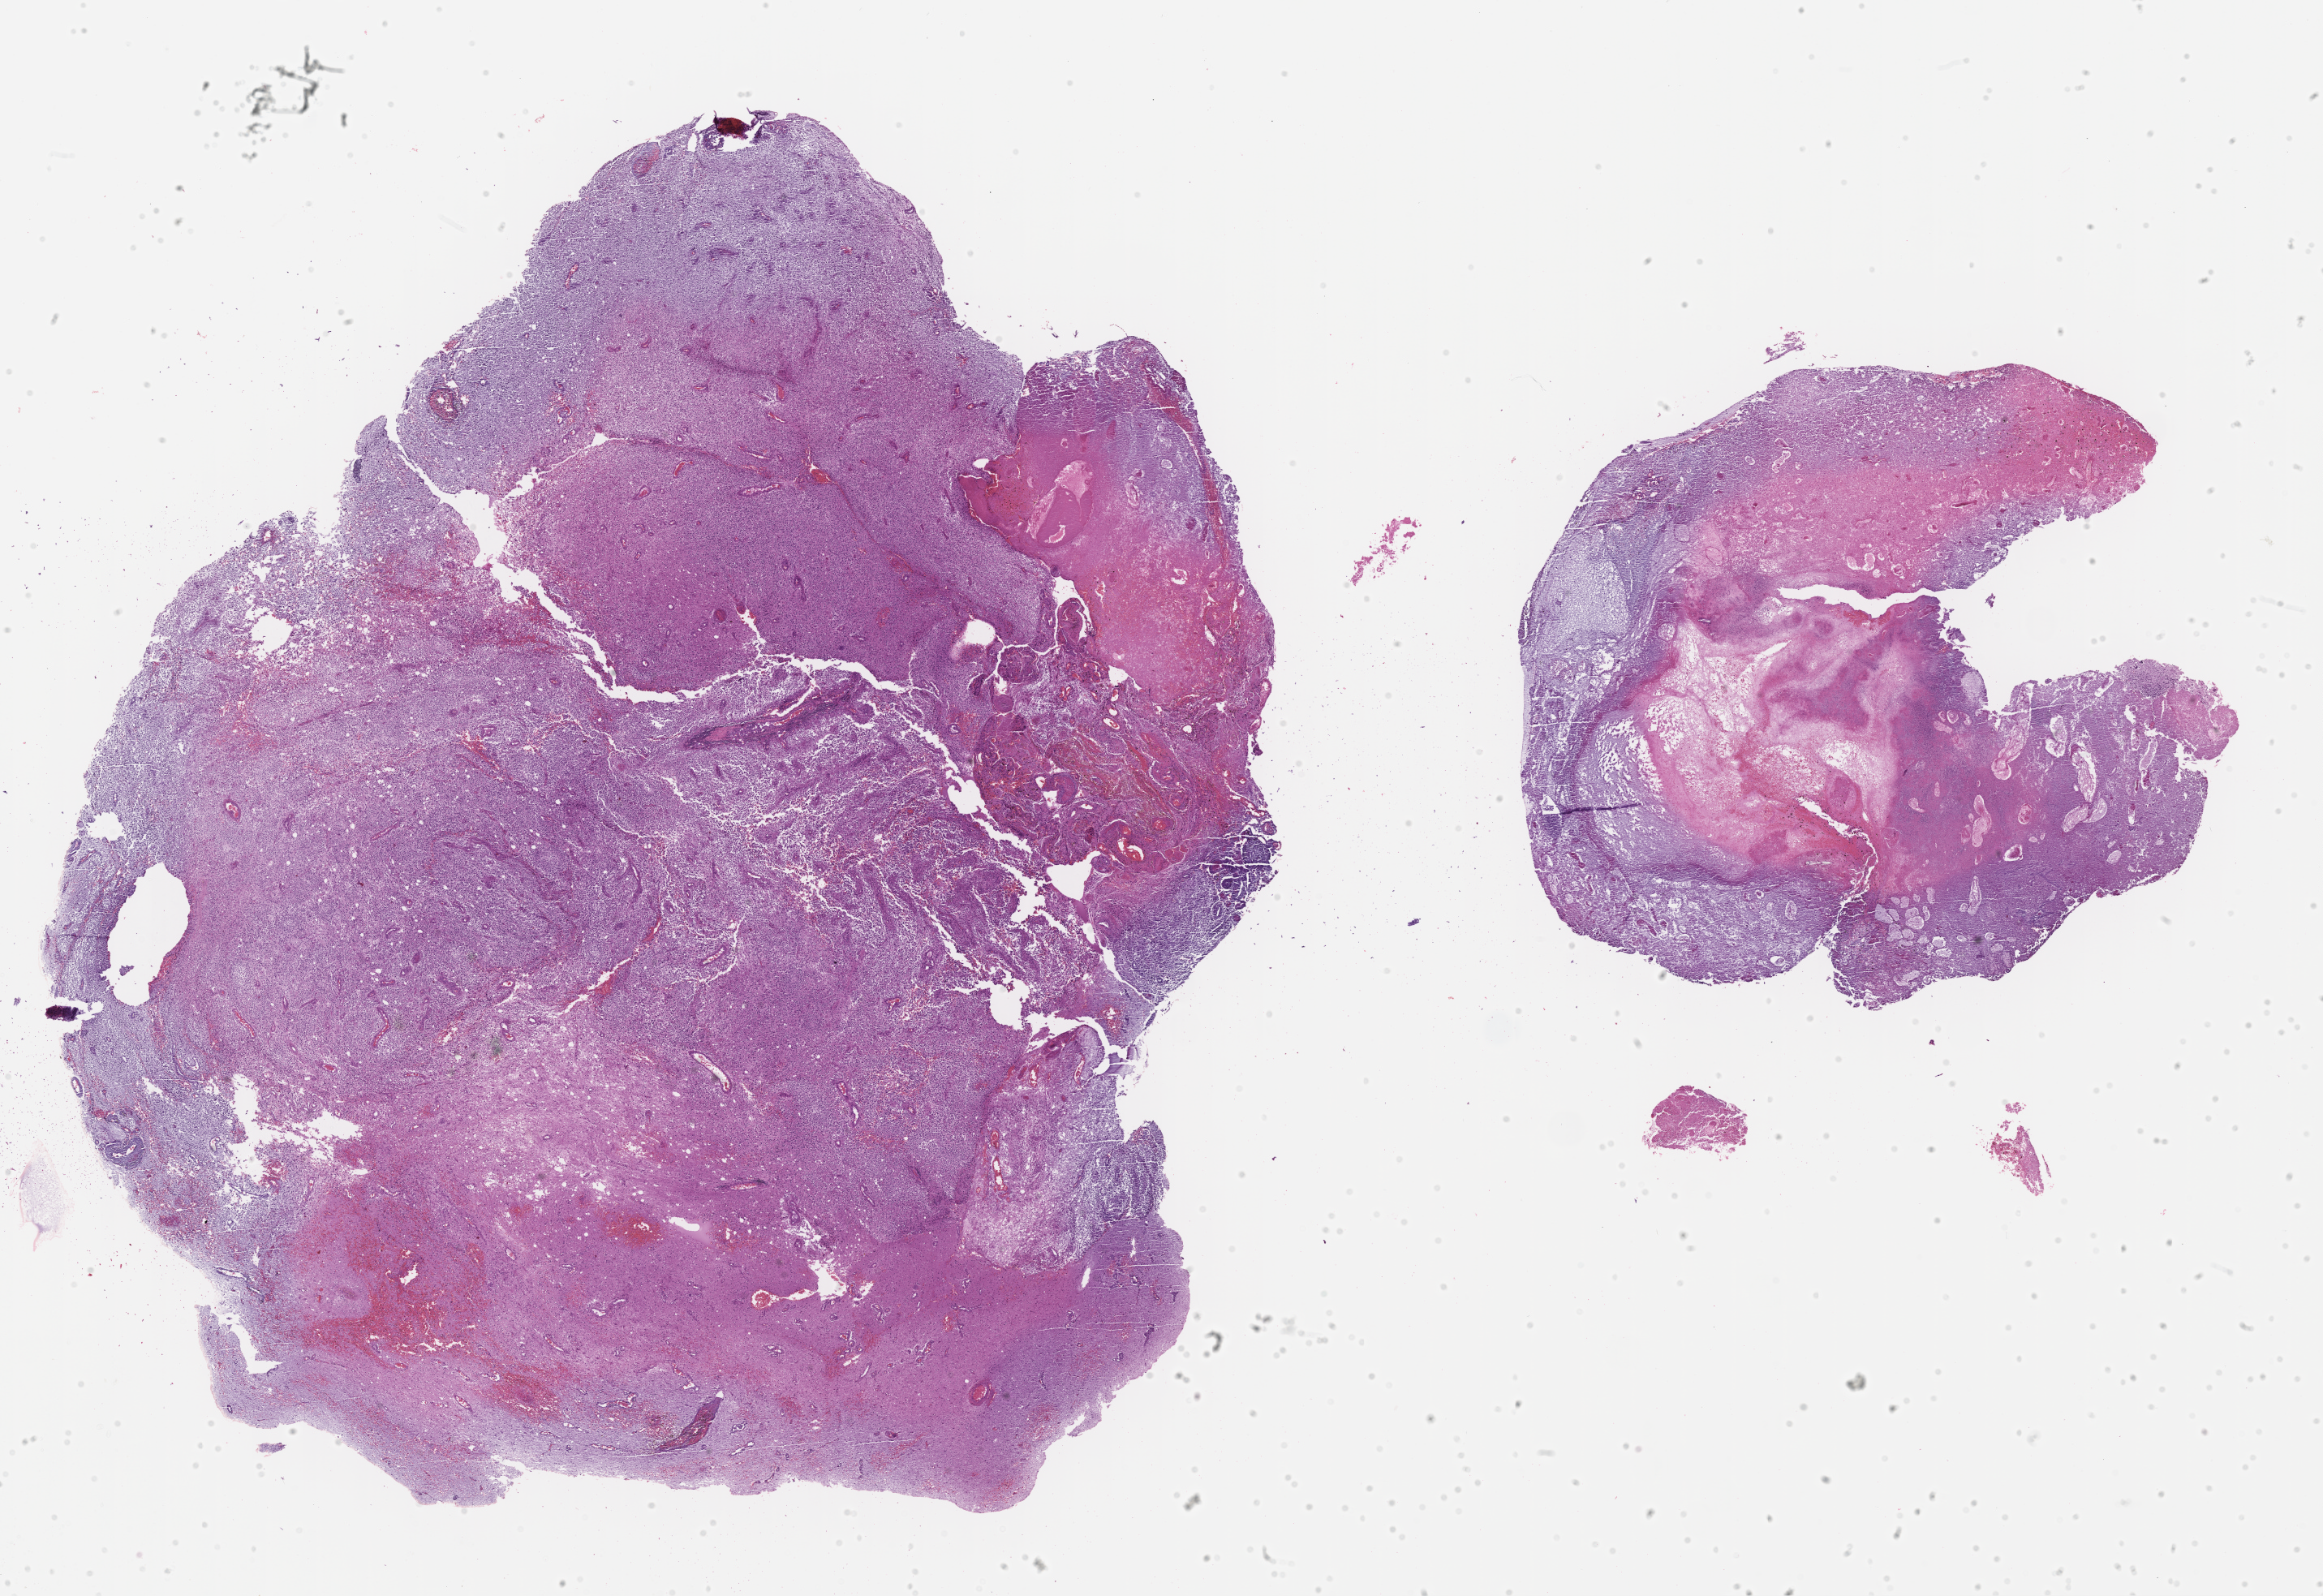
H&E-stained whole-slide image, whole scanned area (about 23.2 x 15.9 mm, slide scanned at 40x) shown as a low-resolution overview. Formalin-fixed paraffin-embedded (FFPE) diagnostic section. Brain, primary tumour sample. Male patient; age at initial diagnosis 62 years.
Pathologic diagnosis: Glioblastoma.